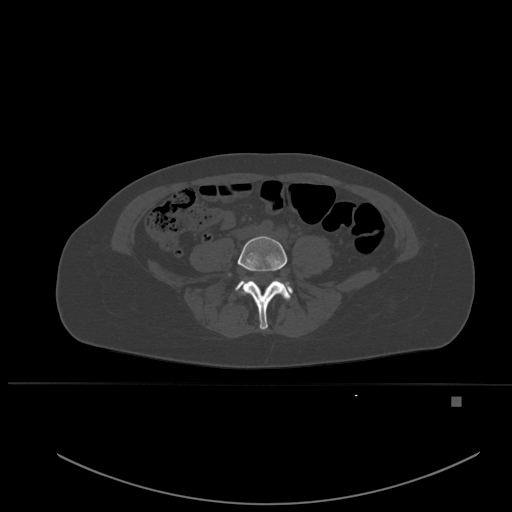
CT including the spine, one axial slice; position 169 of 651 along the scan axis; bone window (W 1800 / L 400 HU); 1.5 mm slice thickness; 512 × 512 image matrix, field of view 443 × 443 mm. Female patient, age 49 years. Case-level facts recorded for this patient, not image findings: primary cancer: breast; vertebrae with lytic lesions (as recorded): L3, T12, L4.
Annotated regions visible in this slice (semi-automatically segmented with operator editing):
- L4 vertebra: bounding box [x1, y1, x2, y2] px = [229, 236, 291, 330]
- L5 vertebra: [236, 281, 293, 294]